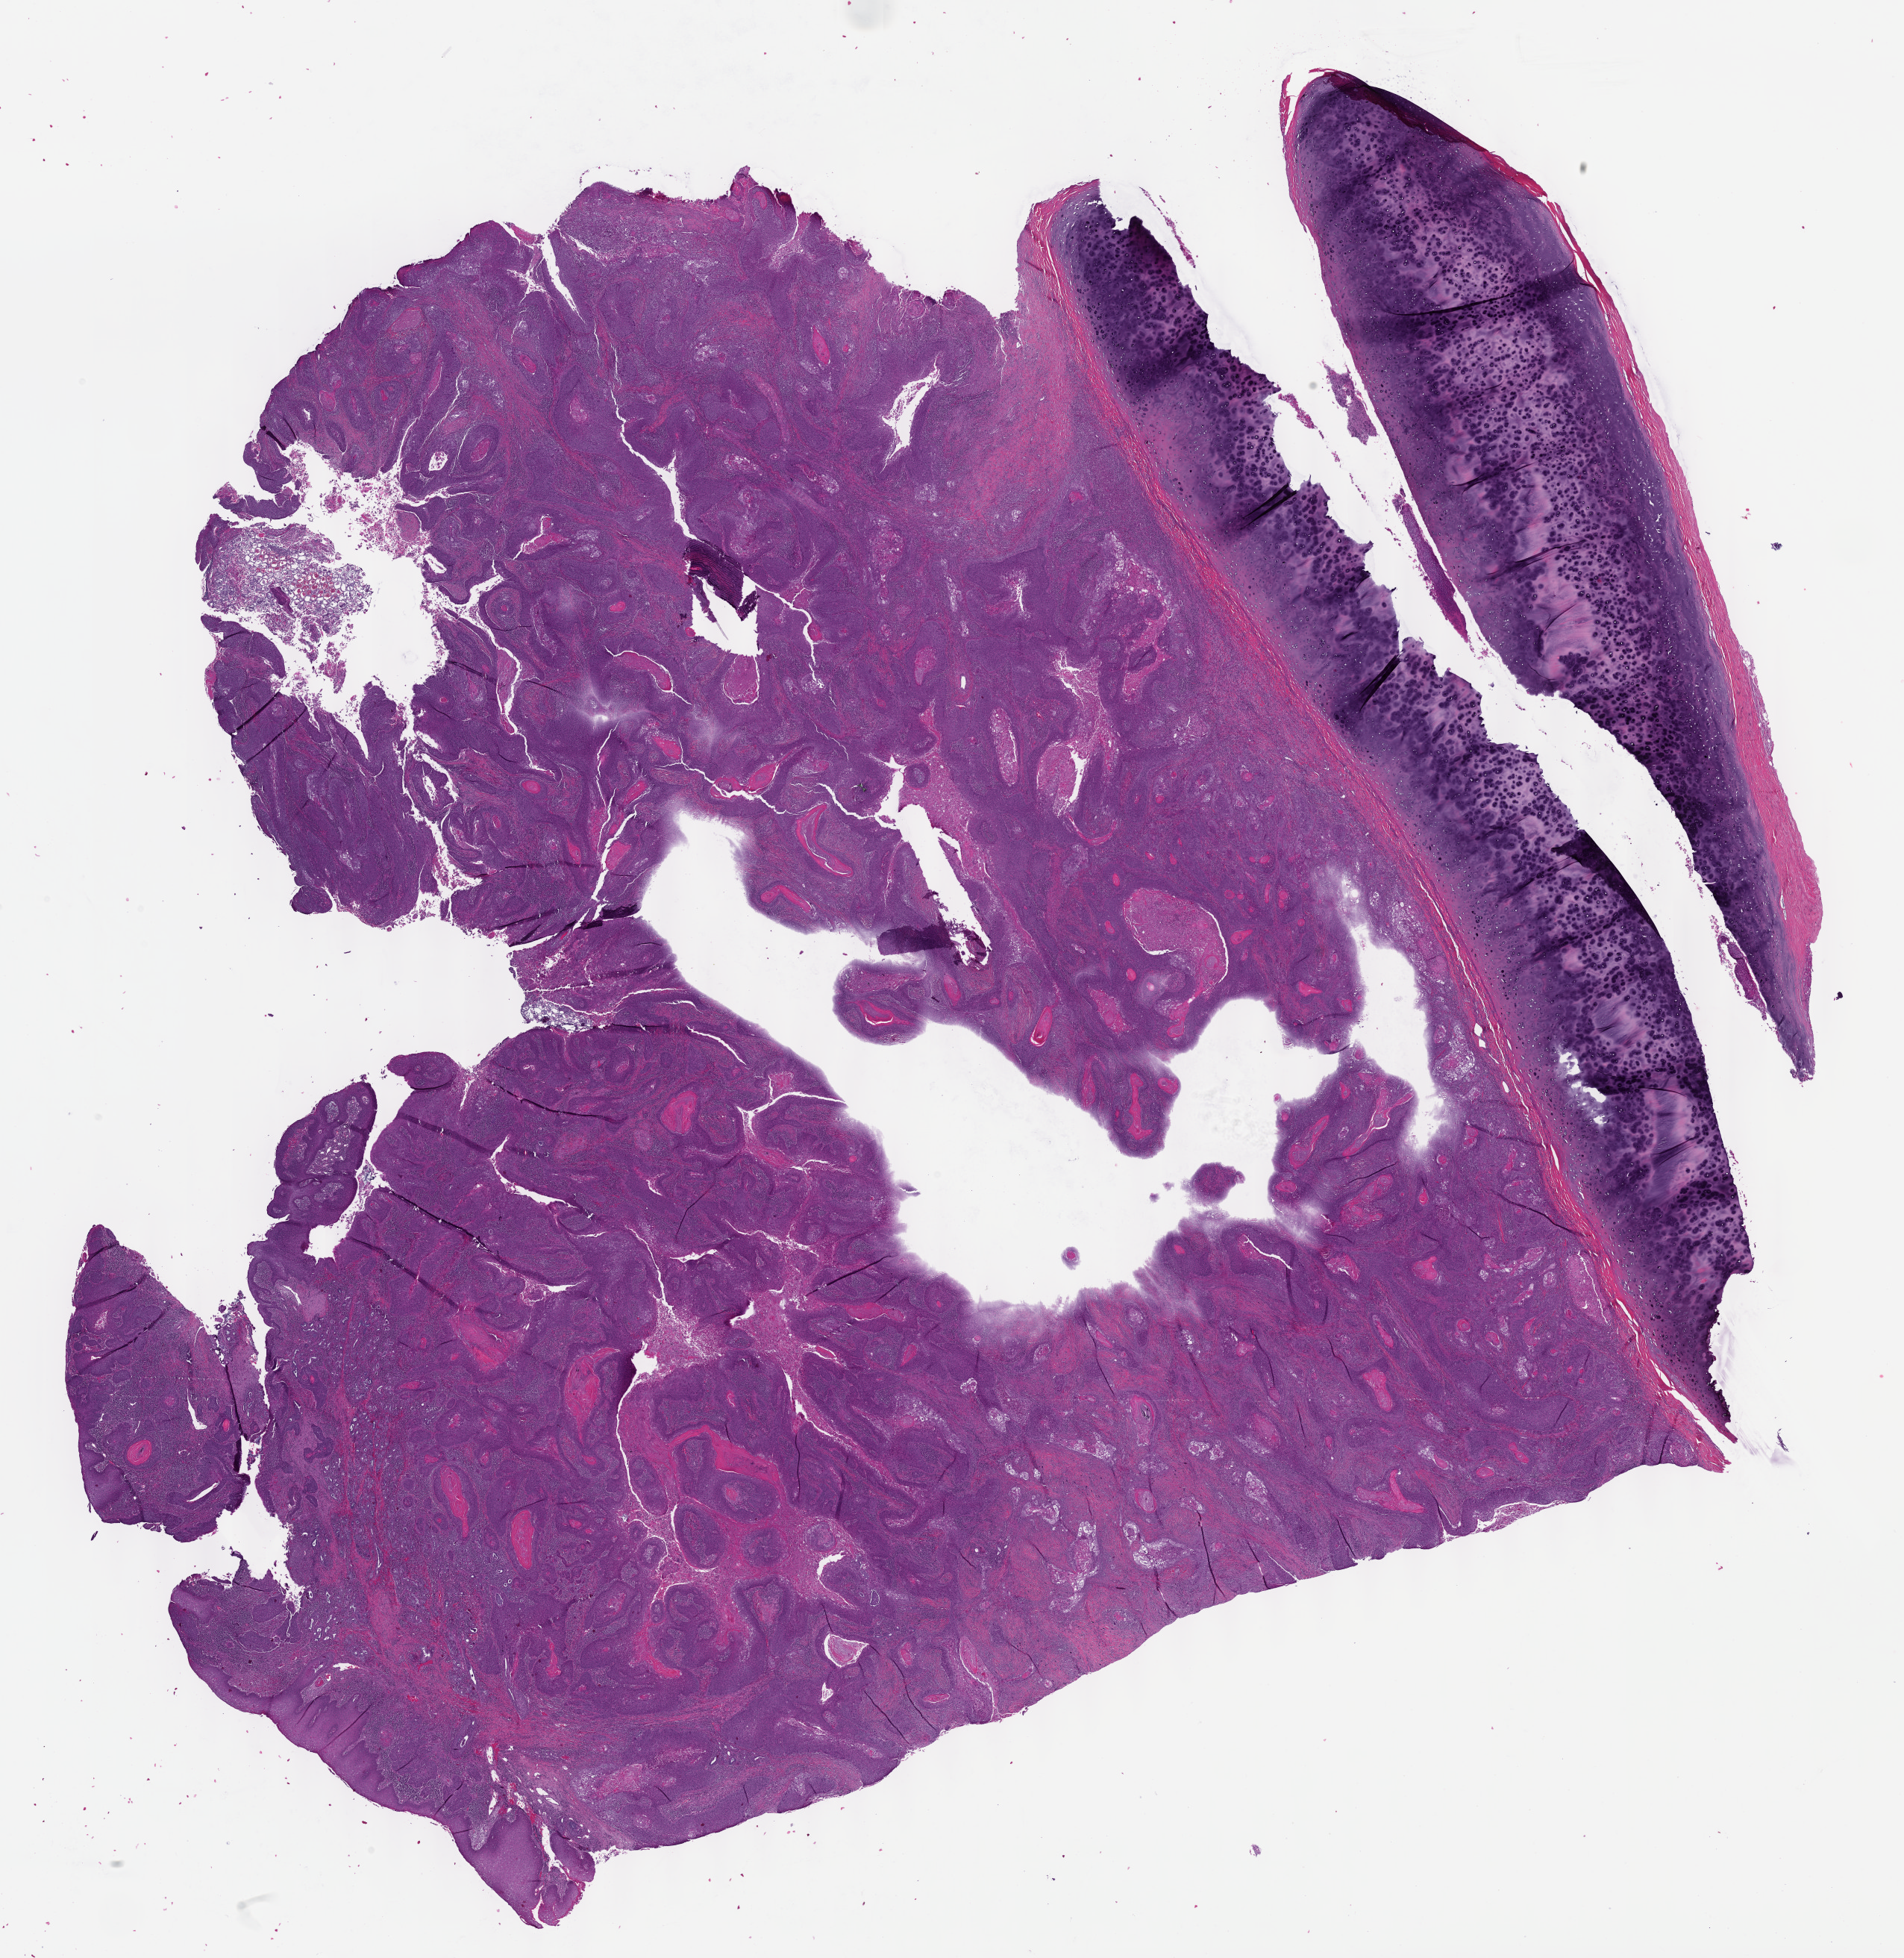
Hematoxylin and eosin (H&E) stained whole-slide image, shown as a low-resolution overview of the whole scanned area (about 20.6 x 21.2 mm, slide scanned at 40x); formalin-fixed paraffin-embedded (FFPE) diagnostic section; primary tumour sample from the head and neck. Female patient; age at initial diagnosis 60 years.
Pathologic diagnosis: Squamous cell carcinoma, NOS.